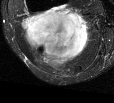
MRI of an extremity soft-tissue mass, one axial slice; position 30 of 44 along the scan axis; T2-weighted fat-saturated; MR volume resampled by the dataset authors to the PET/CT grid (not the native acquisition matrix); 3.27 mm slice thickness; 114 × 103 image matrix. Female patient. From the clinical record (not read from this slice): histological type: liposarcoma; site of the primary tumour: right thigh.
Outlined on this slice (expert contour drawn on MRI and transferred to this co-registered scan by the dataset authors):
- gross tumour volume (mass): bounding box (x1, y1, x2, y2) in pixels: (20, 9, 91, 69)